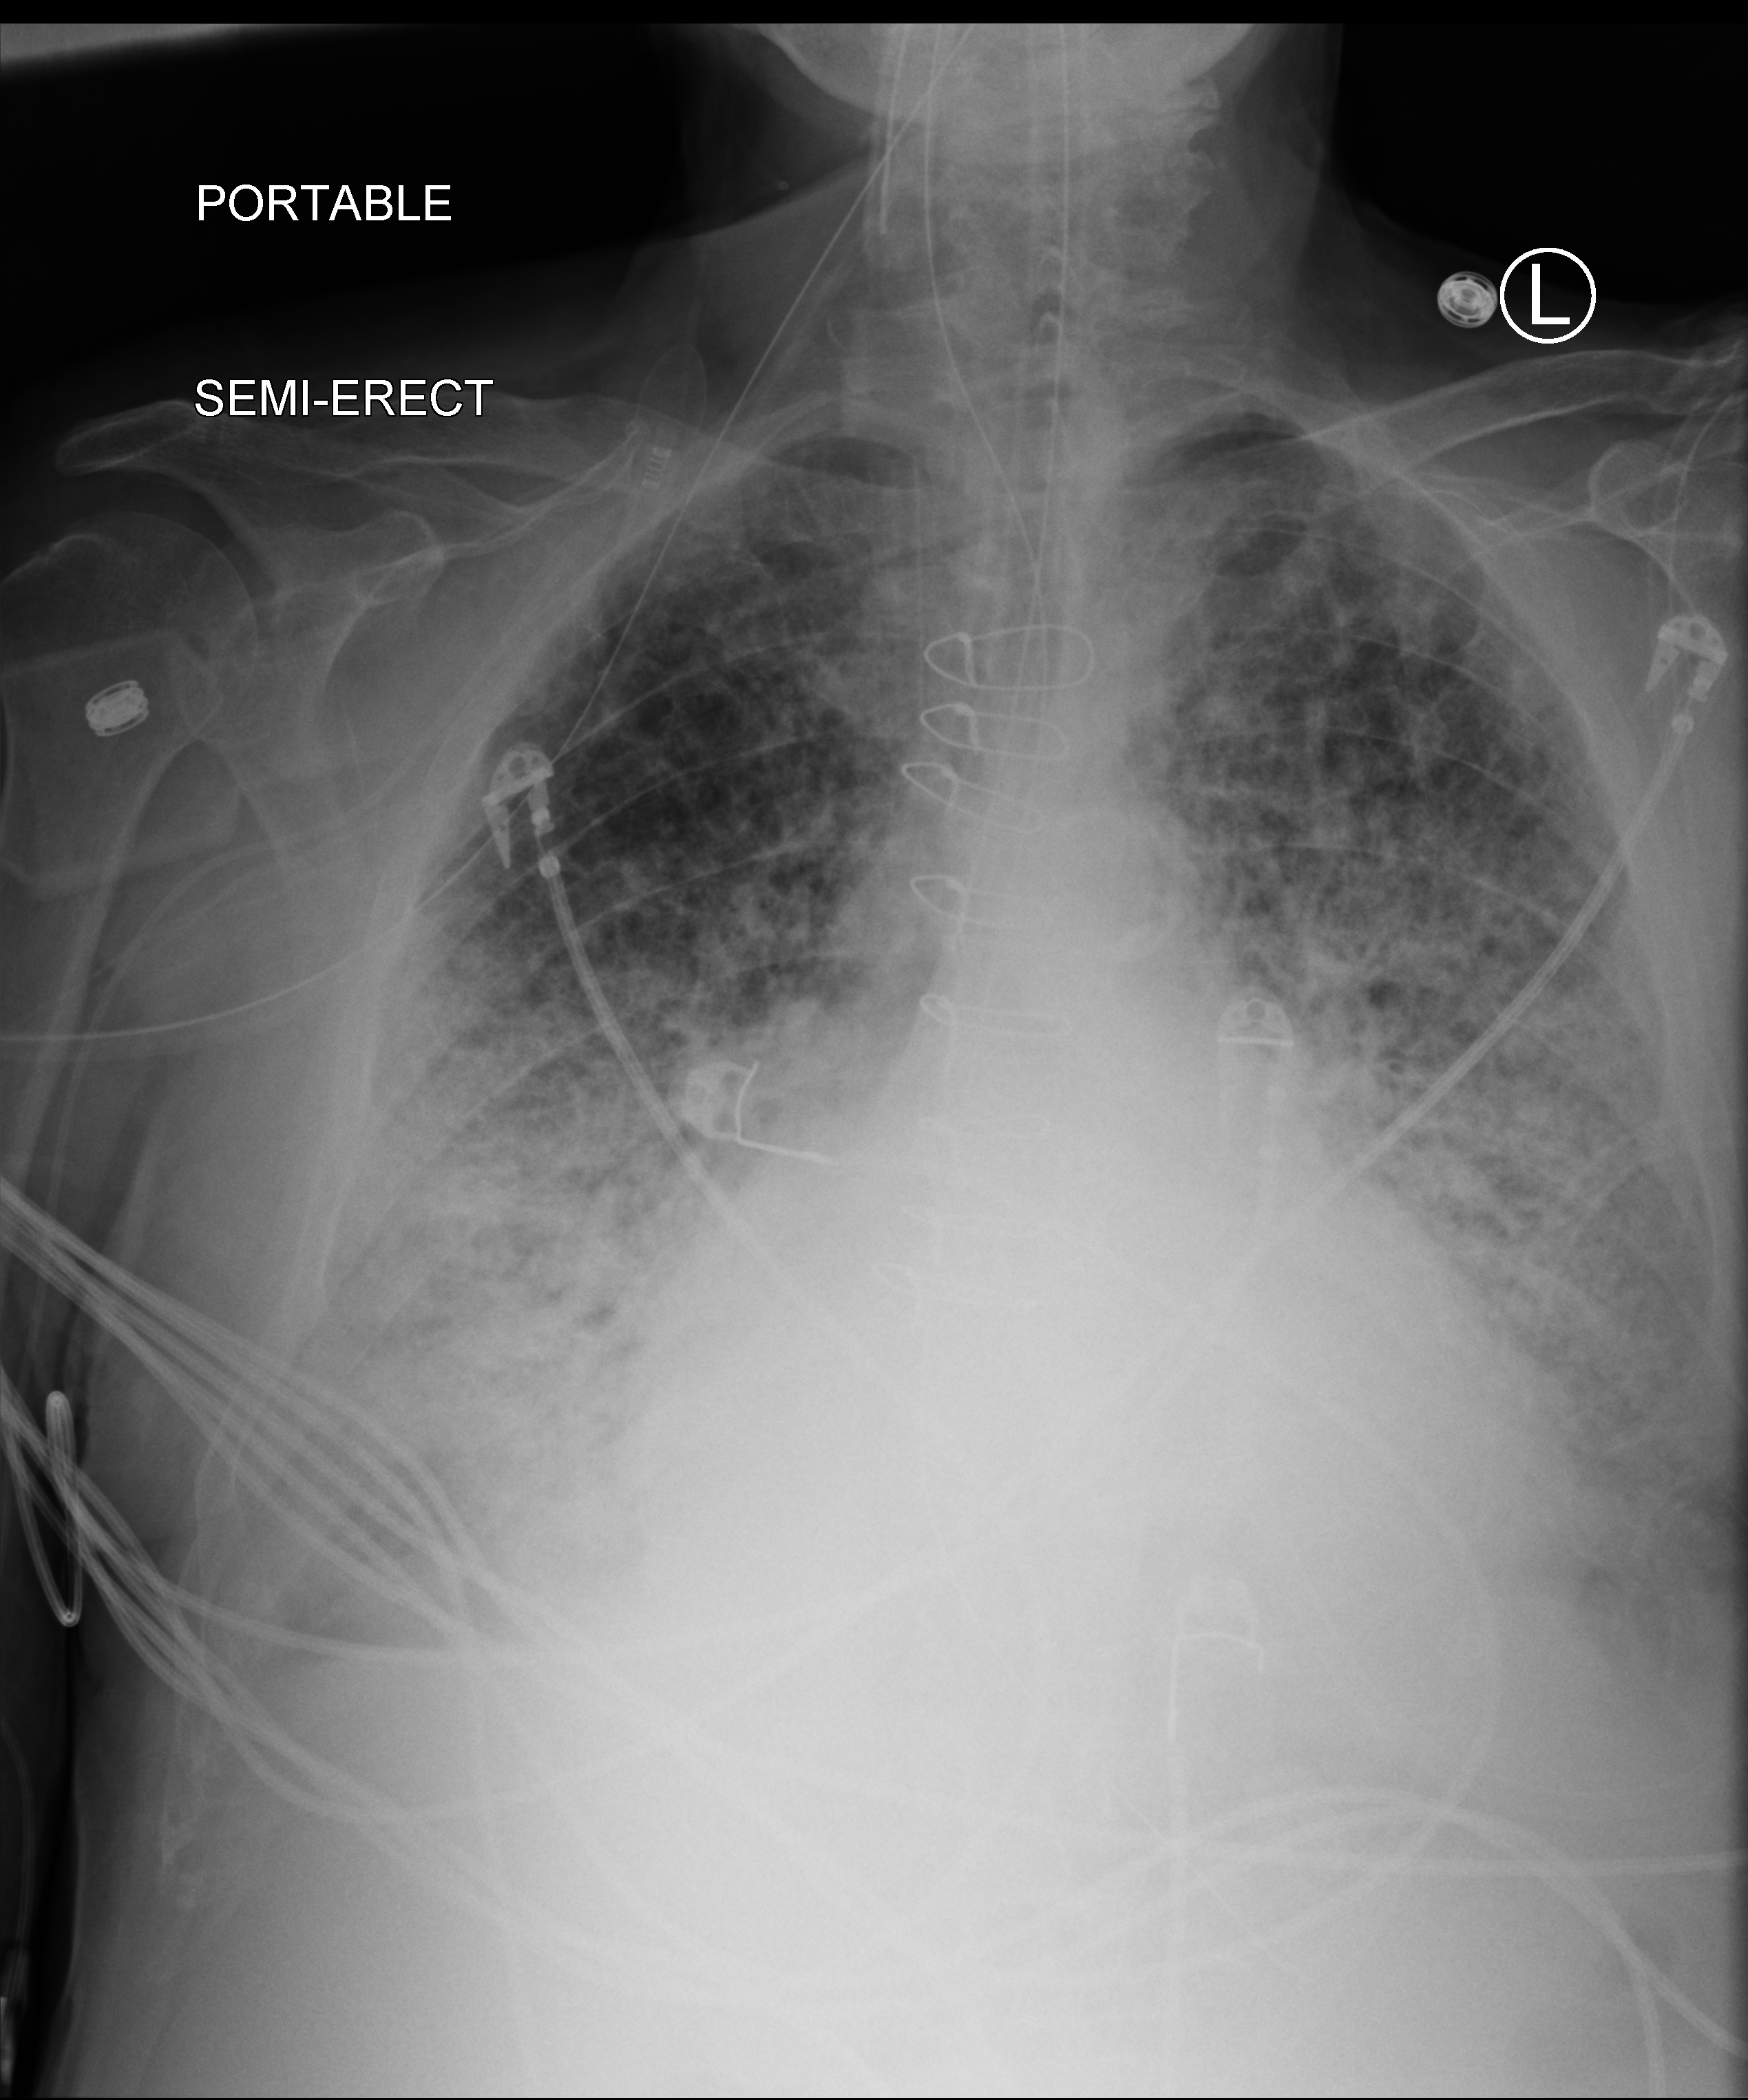
Portable chest radiograph, anteroposterior (AP) projection. Male patient hospitalised with COVID-19, age 75–90 years.
Hospital-stay facts (about this admission, not read from this image; timing relative to this image not recorded): mechanically ventilated during this hospital stay: yes; admitted to intensive care during this hospital stay: yes.